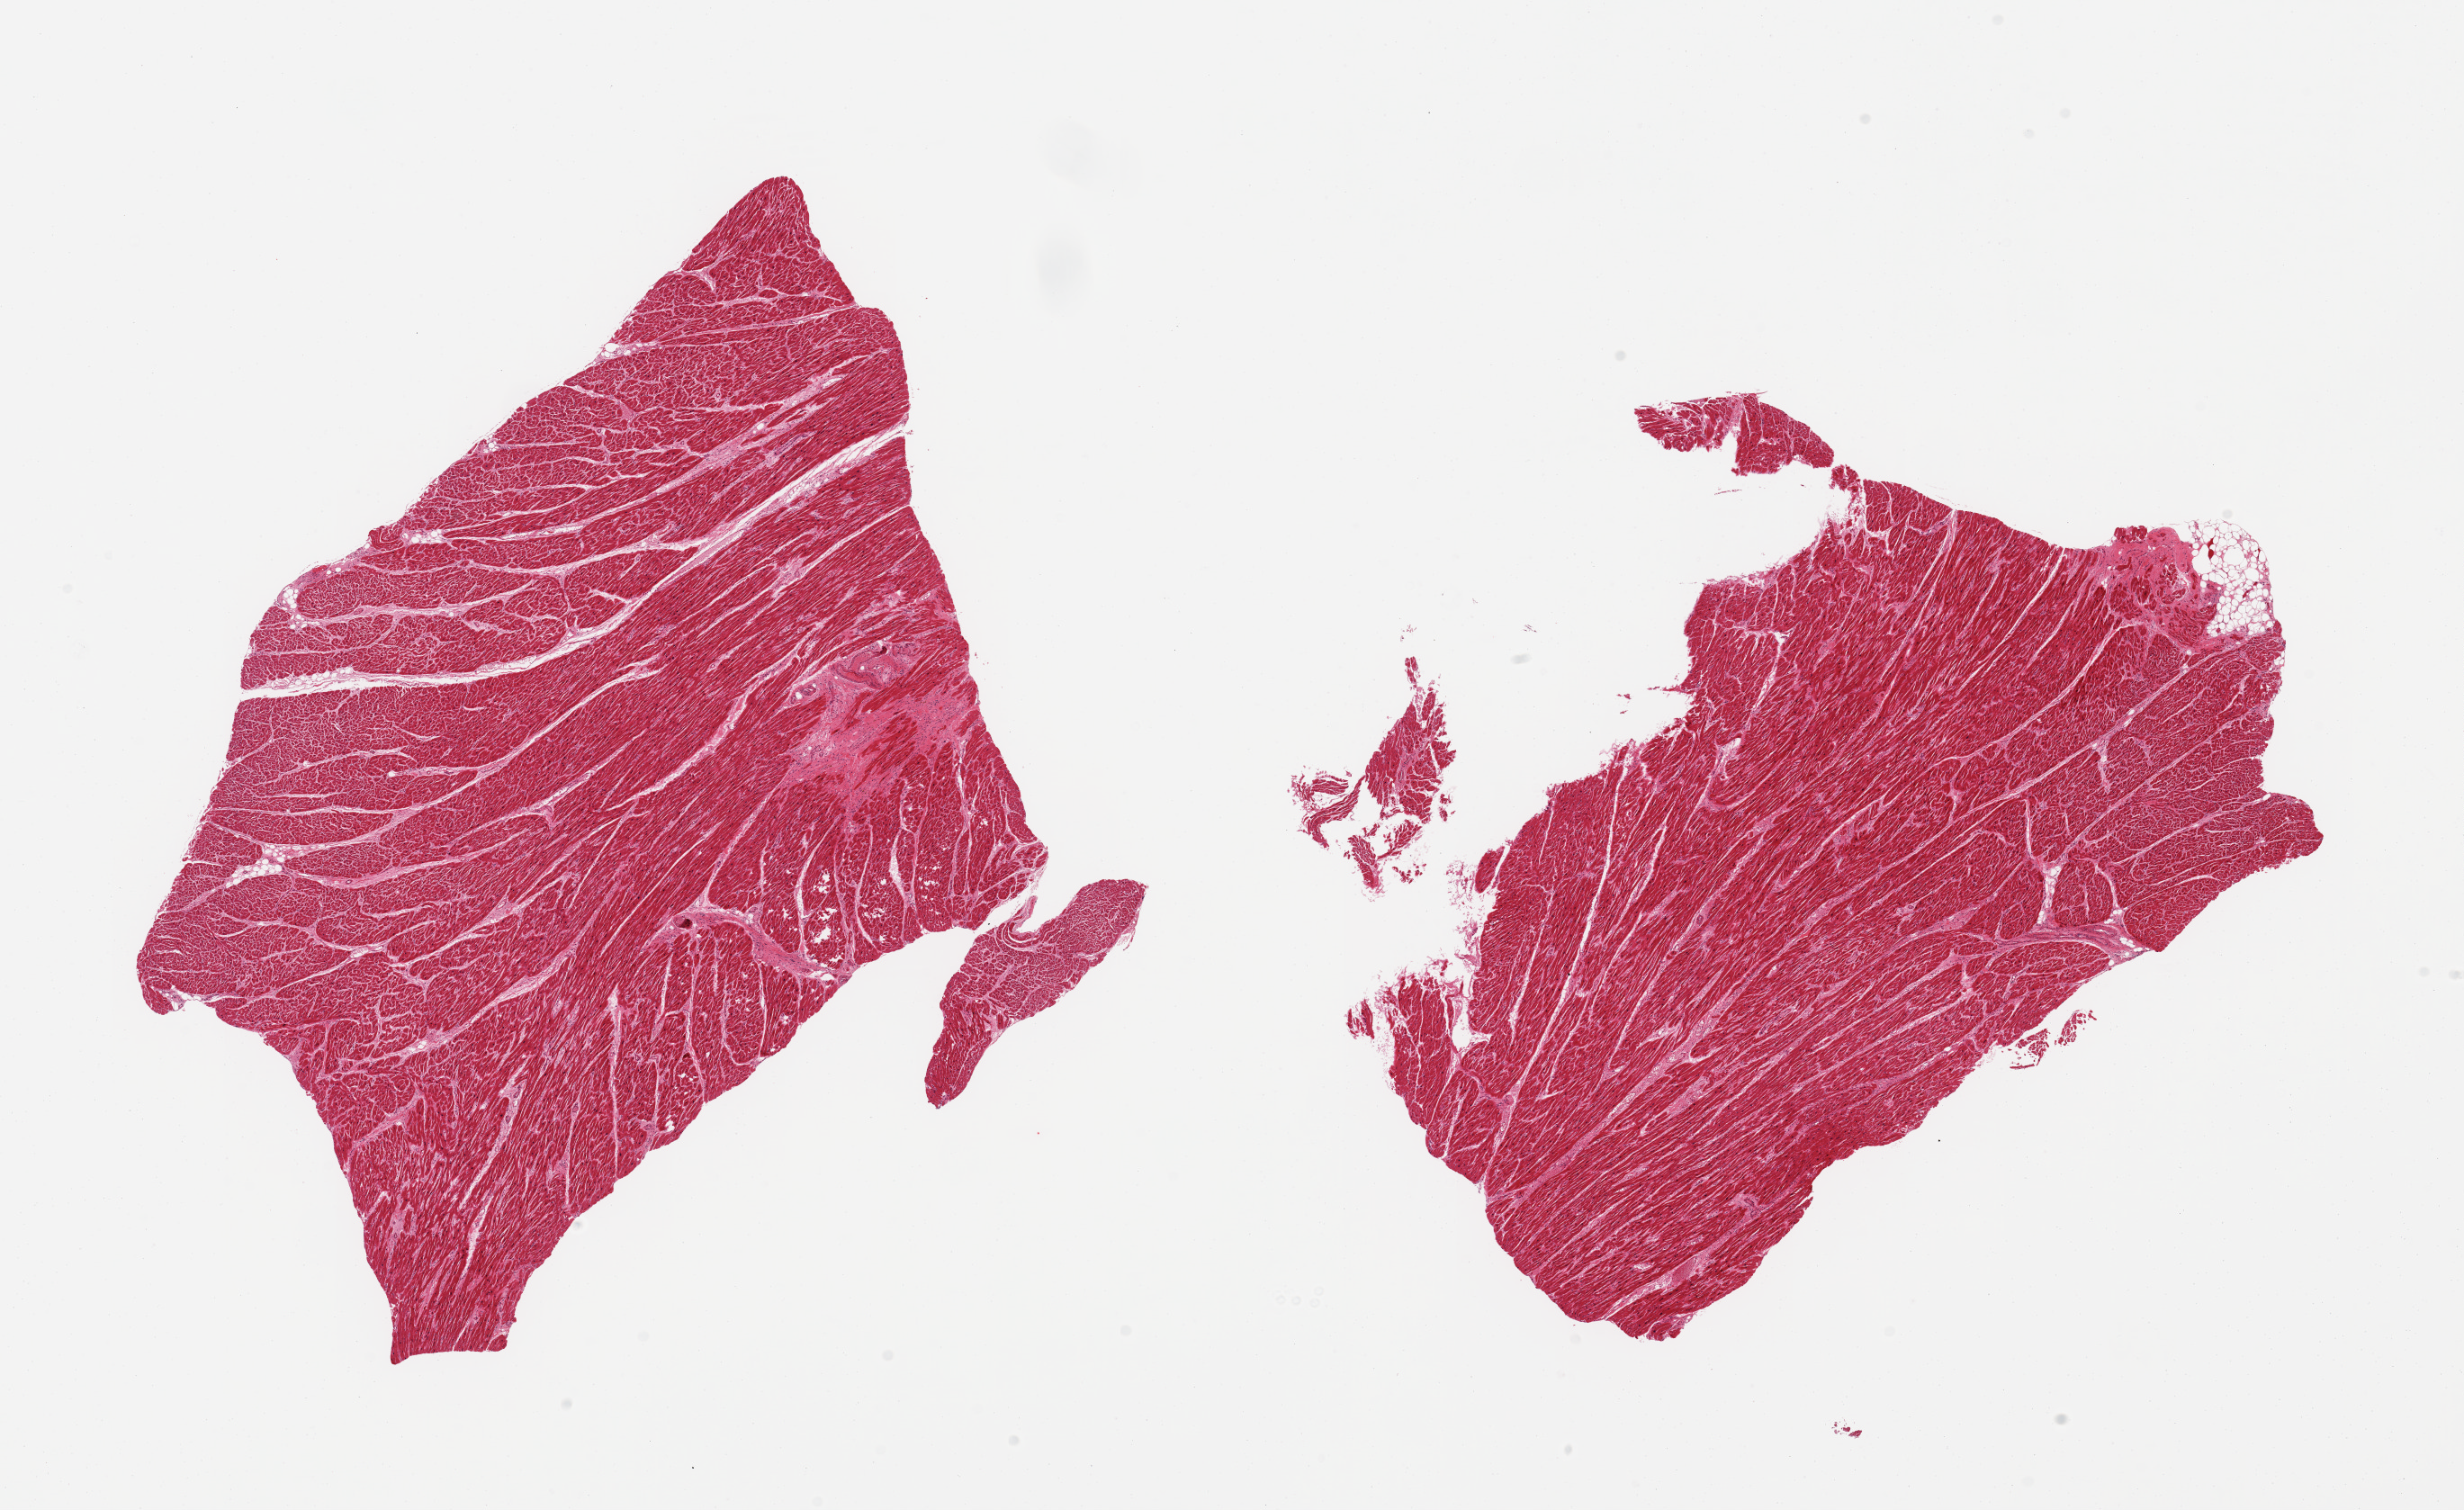
H&E whole-slide image — a low-resolution overview of the entire scanned area, about 21.7 x 13.3 mm. PAXgene-fixed paraffin-embedded (PFPE) section. Section of heart (target tissue). Donor tissue sample.
Reviewer comment on this tissue sample: 2 pieces, moderate ischemic damage, microinfarct (~1.5mm) noted.